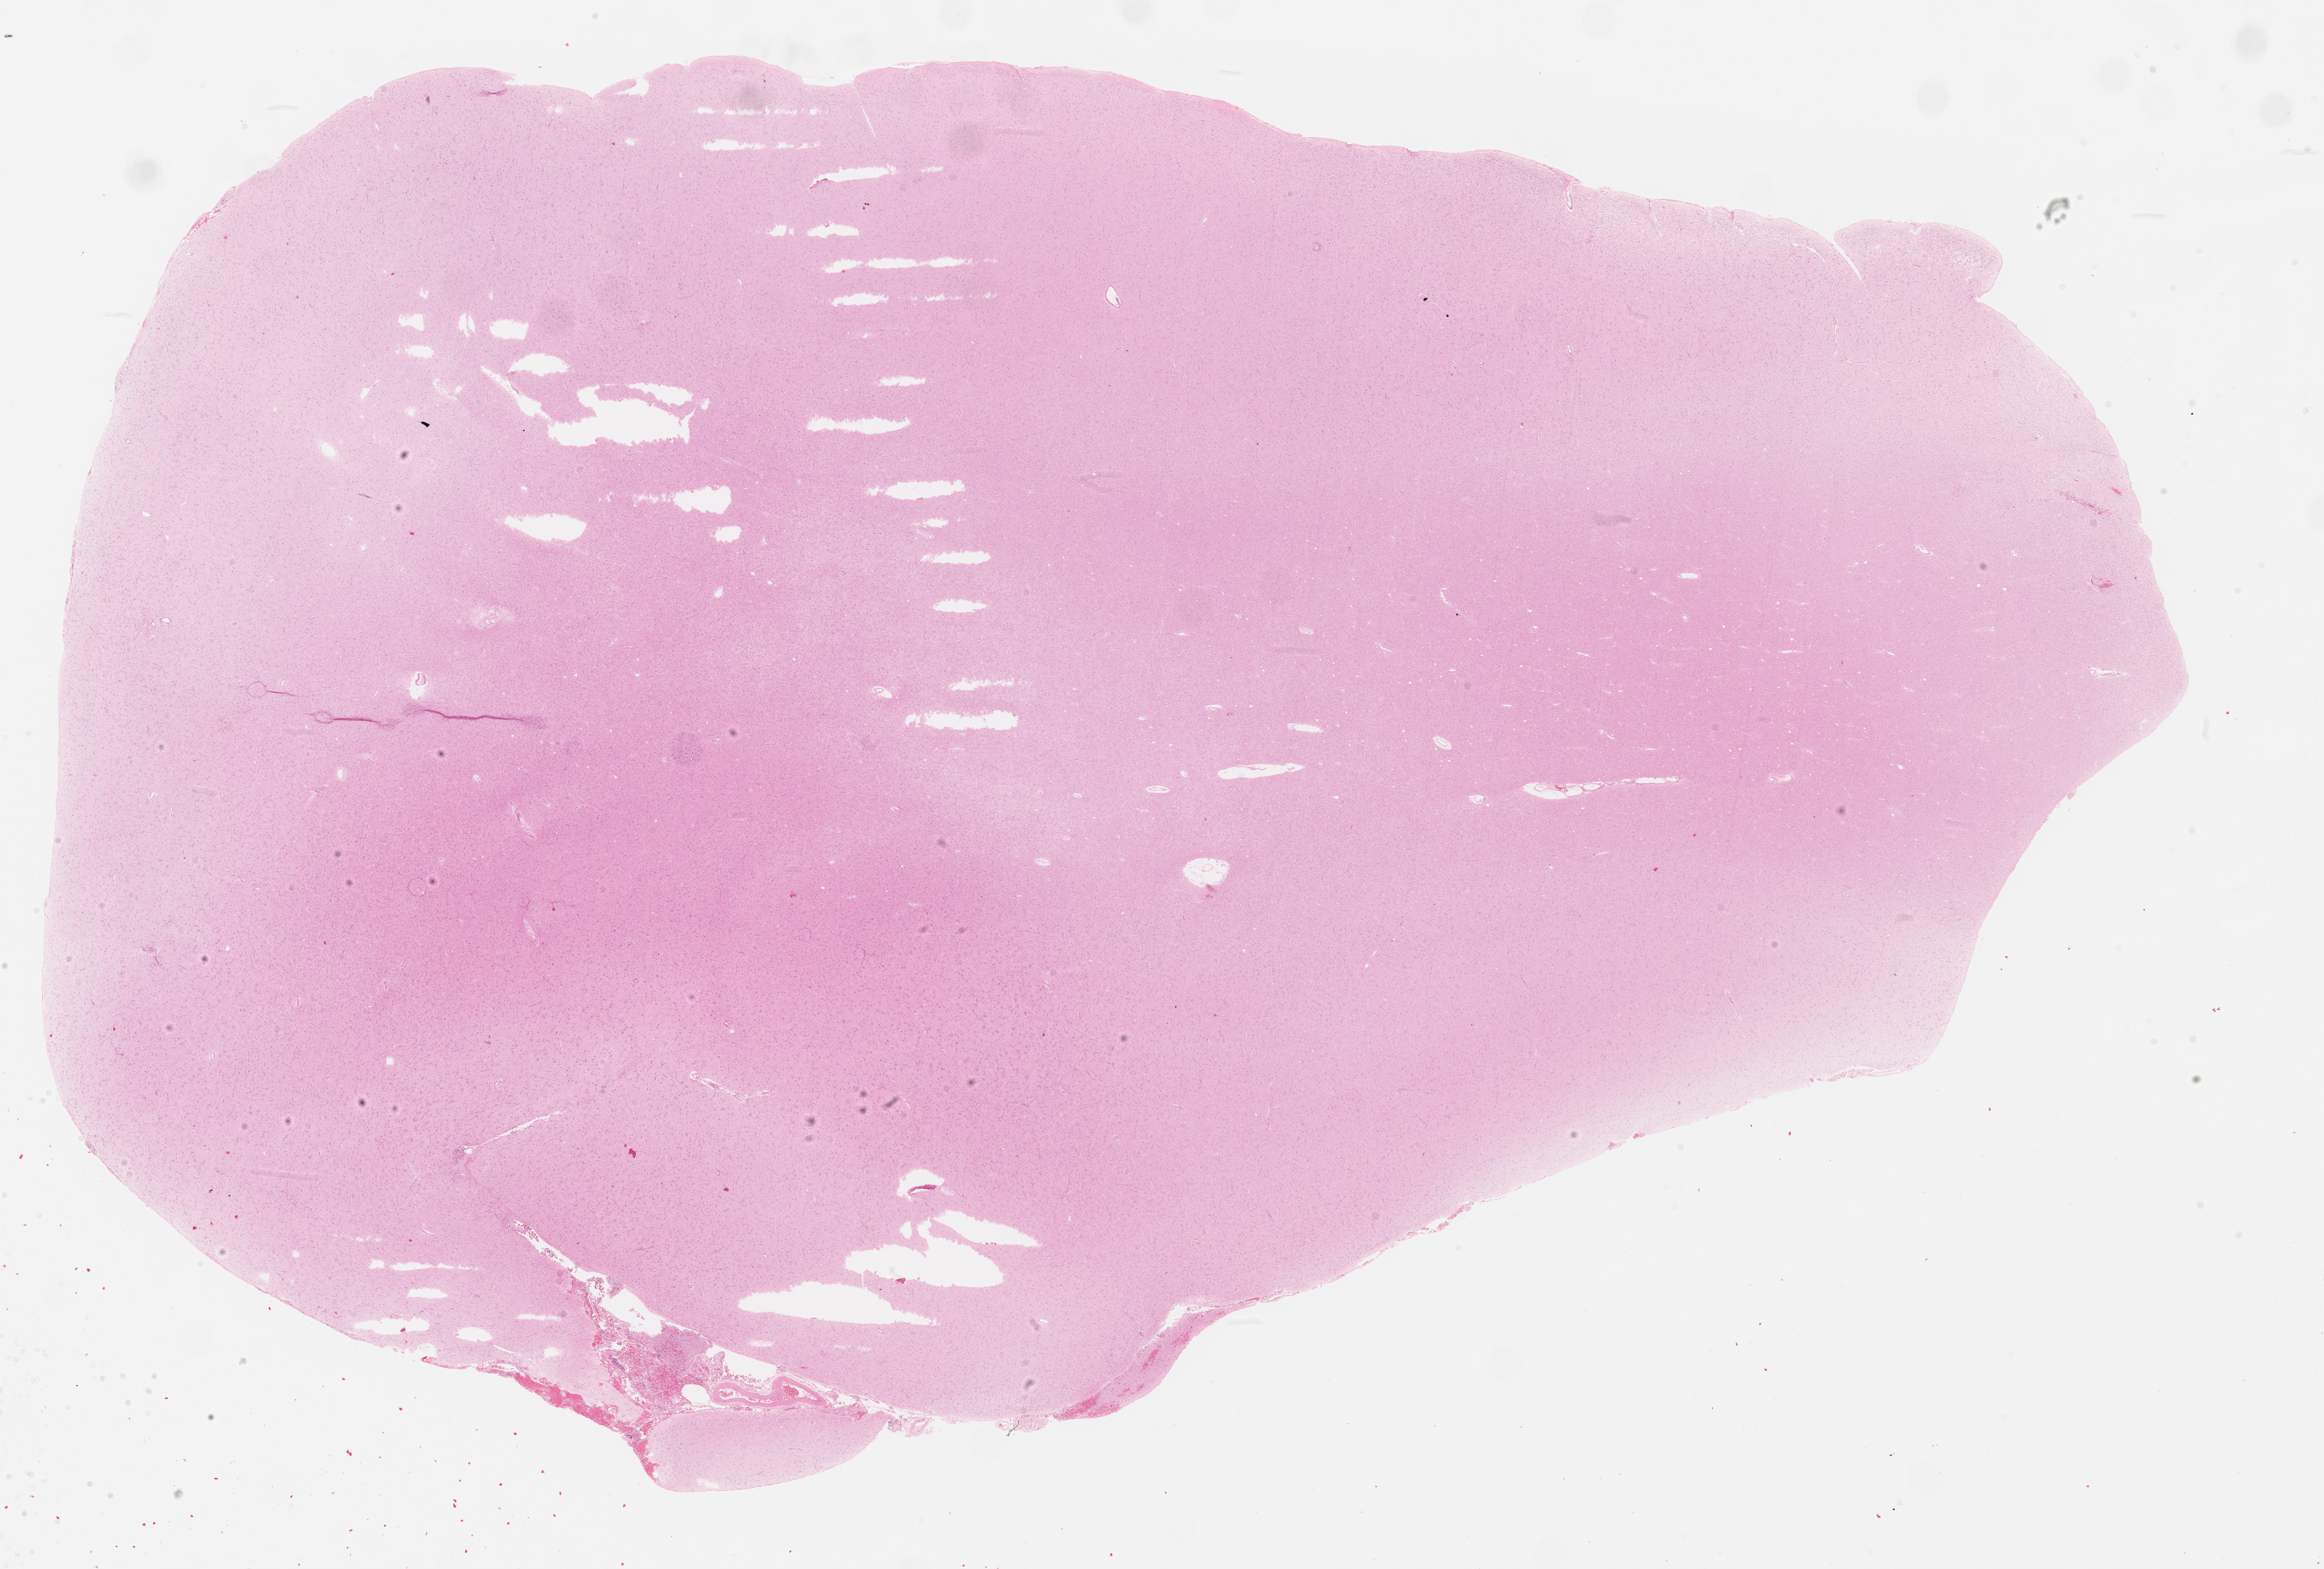
Digitized Hematoxylin and eosin (H&E) stained tissue section (whole slide) — shown as a low-resolution overview of the whole scanned area (about 24.4 x 16.5 mm); FFPE section; sample: primary tumour, brain. Patient: male, age at initial diagnosis 40 years. Histologic grade: G2 (moderately differentiated).
• histologic diagnosis: Oligodendroglioma, NOS (cerebrum)
• laterality: right